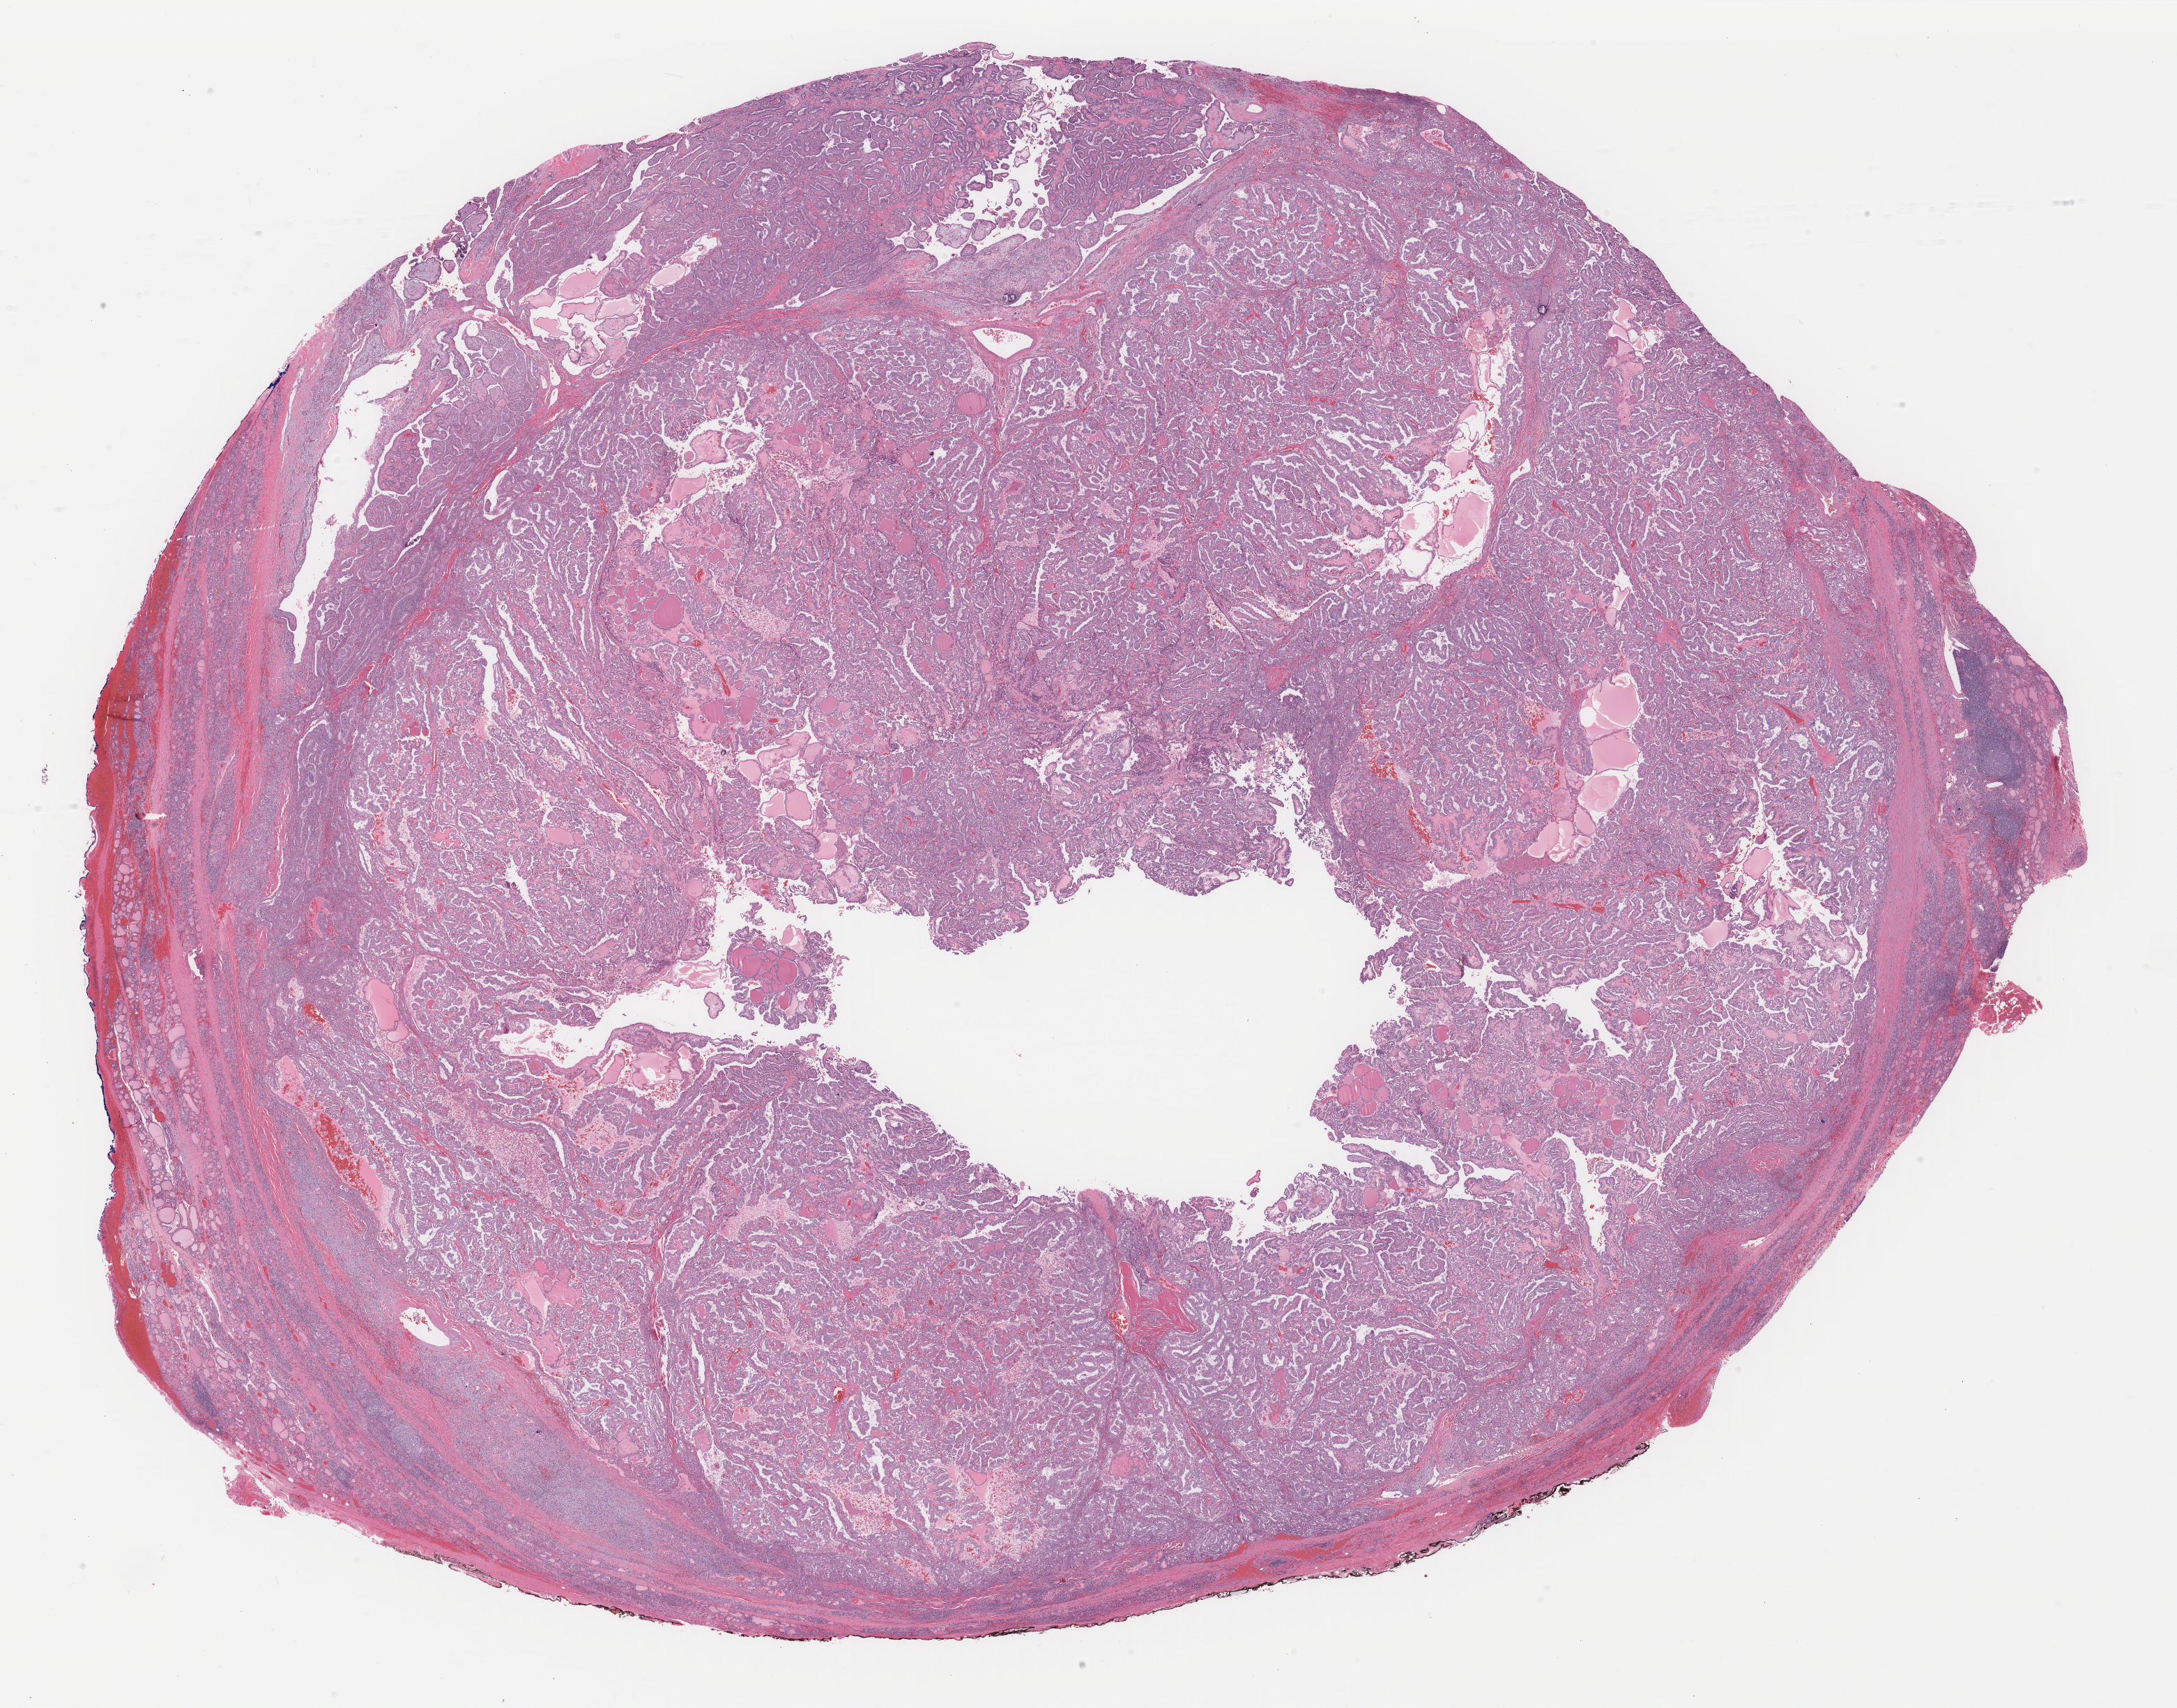
Digitized Hematoxylin and eosin (H&E) stained tissue section (whole slide), a low-resolution overview of the entire scanned area, about 24.8 x 19.4 mm (acquisition: 40x scan). FFPE section. Primary tumour sample from the thyroid. Patient: female, age at initial diagnosis 37 years.
Laterality: right. Histologic diagnosis: Papillary adenocarcinoma, NOS. TNM: T2 N0 M0. AJCC pathologic stage: I (7th edition).